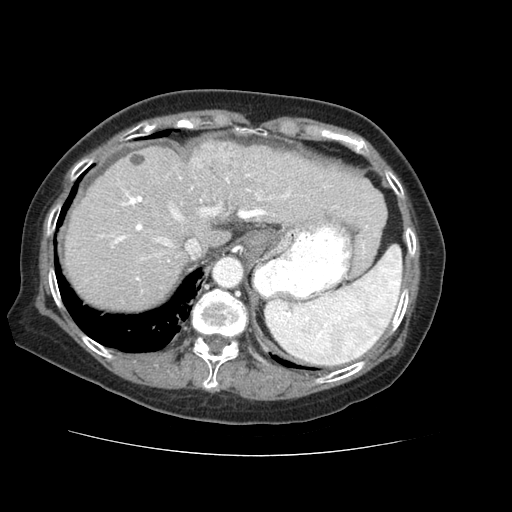
Contrast-enhanced abdominal CT (liver protocol), one axial slice. Slice 49 of 73 in the series (ordered by position). 120 kVp. Soft-tissue window (W 400 / L 40 HU). 2.5 mm slice thickness. 512 × 512 image matrix, field of view 360 × 360 mm. From the clinical record (not read from this slice): diagnosis: hepatocellular carcinoma (patient treated with transarterial chemoembolisation; whether this scan precedes or follows treatment is not stated here); TNM stage (as recorded): Stage-IVB; Child-Pugh class: A; tumour differentiation: well differentiated.
Structures marked on this image (semi-automatically segmented with operator editing):
- abdominal aorta: bounding box <214,257,242,286> (left, top, right, bottom; pixels)
- liver parenchyma outside the tumour (the mass and vessels are separate outlines, so this box may not span the whole liver): <64,140,380,310>
- mass: <187,140,242,183>
- liver vessels: <100,174,291,281>